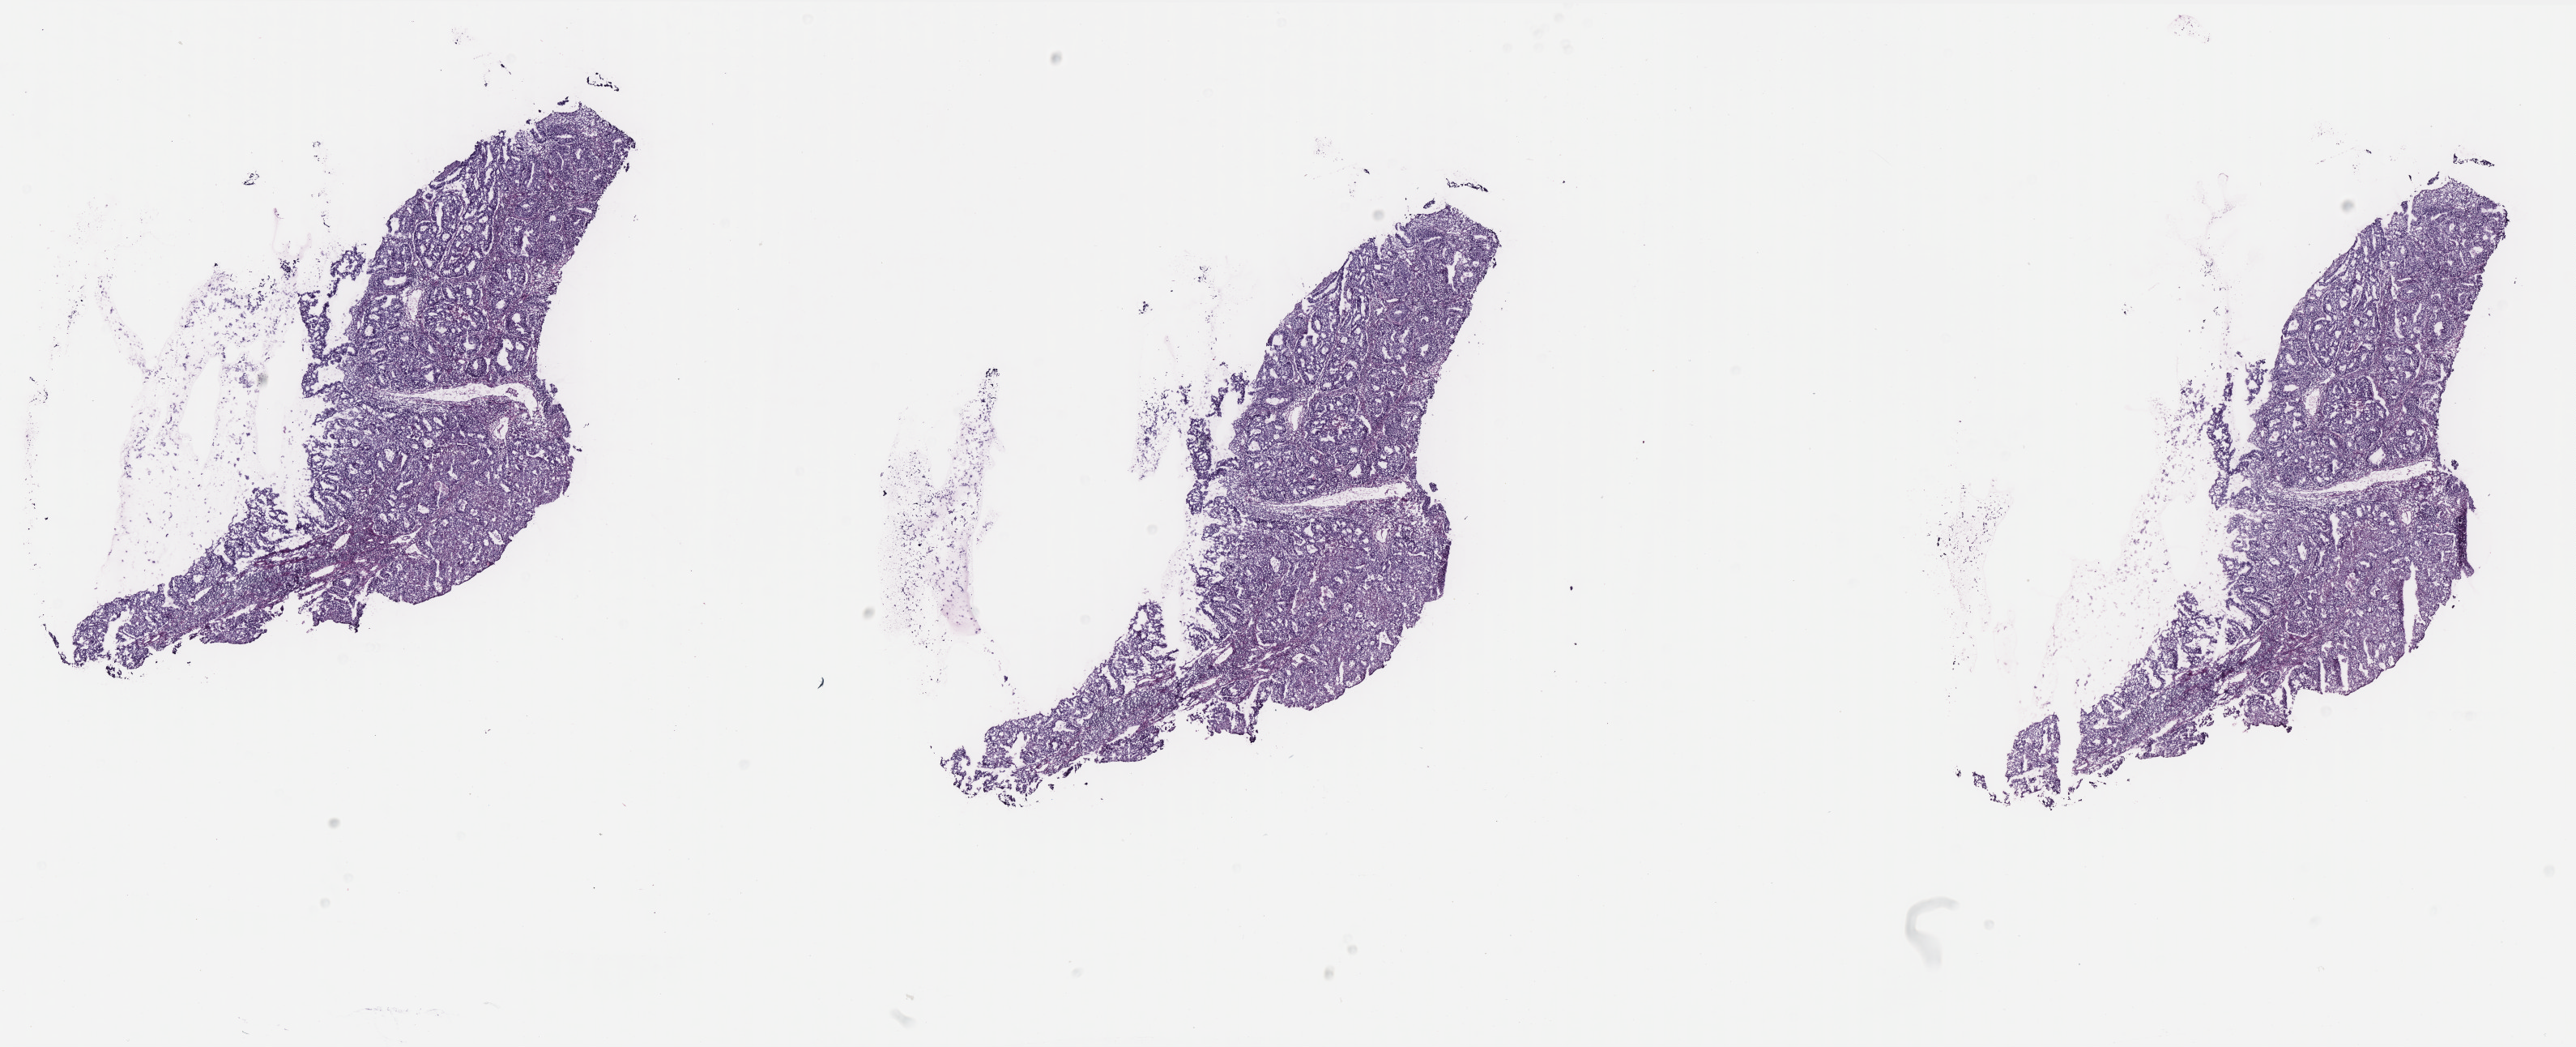
Whole-slide histology image, Hematoxylin and eosin (H&E) stained, a low-resolution overview of the entire scanned area, about 25.5 x 10.4 mm; frozen section from the bottom of the tissue portion; primary tumour sample from the uterus. Female patient; age at initial diagnosis 38 years. Histologic grade: G2 (moderately differentiated). Composition of this section per pathologist review: tumour cells 75%, tumour nuclei 85%, normal cells 10%, stromal cells 5%, necrosis 10%. Infiltration values recorded for this section: lymphocyte infiltration 60%, monocyte infiltration 0%, neutrophil infiltration 30%.
Pathologic diagnosis: Endometrioid adenocarcinoma, NOS (endometrium). FIGO stage: IA. Lymph nodes positive (case pathology): 0 of 5 examined.